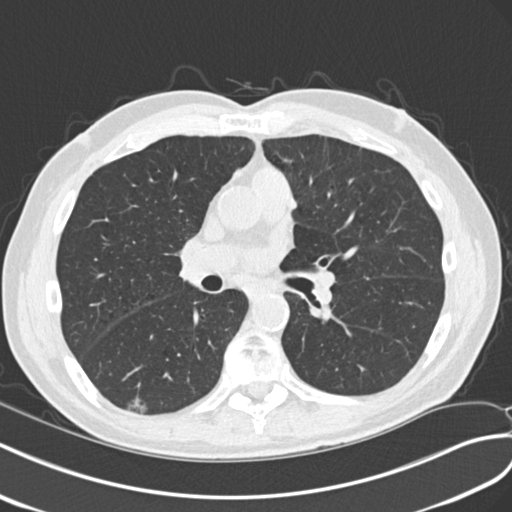
Low-dose screening chest CT, axial slice; second annual screen; lung window (W 1500 / L -600 HU); standard (soft-tissue) reconstruction kernel (B30f); slice 106 of 240 in the series; 512 × 512 image matrix. Male, age 68 years at enrolment. Current smoker at enrolment.
Expert reader's lesion annotation, bounding box (x1, y1, x2, y2) in pixels: (109, 384, 159, 421). The screening reader recorded 4 non-calcified nodules or masses ≥4 mm on this exam (right upper lobe, left upper lobe, right upper lobe, right lower lobe); which of them this box marks is not recorded. Official screen result: positive, other. Lung cancer was diagnosed 653 days after this screen: non-small cell carcinoma, right lower lobe, poorly differentiated (G3), stage IA (AJCC 6th edition), 23 mm at pathology.